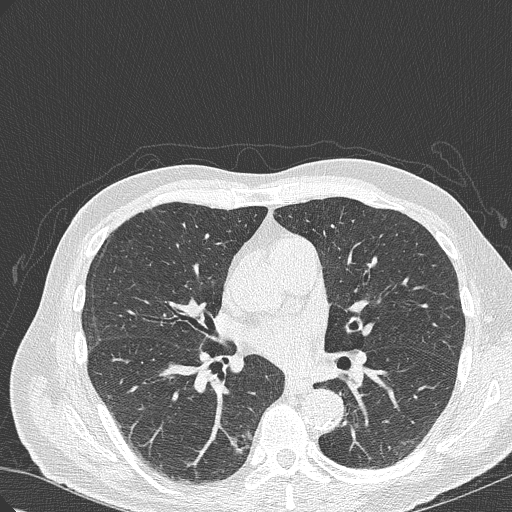
Low-dose screening chest CT, axial slice. Baseline annual screen. Lung window (W 1500 / L -600 HU). 120 kVp. 512 × 512 image matrix, field of view 350 × 350 mm. Male participant, aged 70 years at enrolment.
Expert-annotated lung lesion, box from (x=197, y=420) to (x=260, y=482) px. The screening reader recorded 4 non-calcified nodules or masses ≥4 mm on this exam; which of them this box marks is not recorded. Official screen result: positive, change unspecified: nodule(s) >= 4 mm or enlarging nodule(s), mass(es), or other non-specific abnormalities suspicious for lung cancer. Later outcome: lung cancer diagnosed 978 days after this screen (after the third annual screen) — bronchiolo-alveolar adenocarcinoma, NOS, right lower lobe, poorly differentiated (G3), stage IB (AJCC 6th edition), 30 mm at pathology.